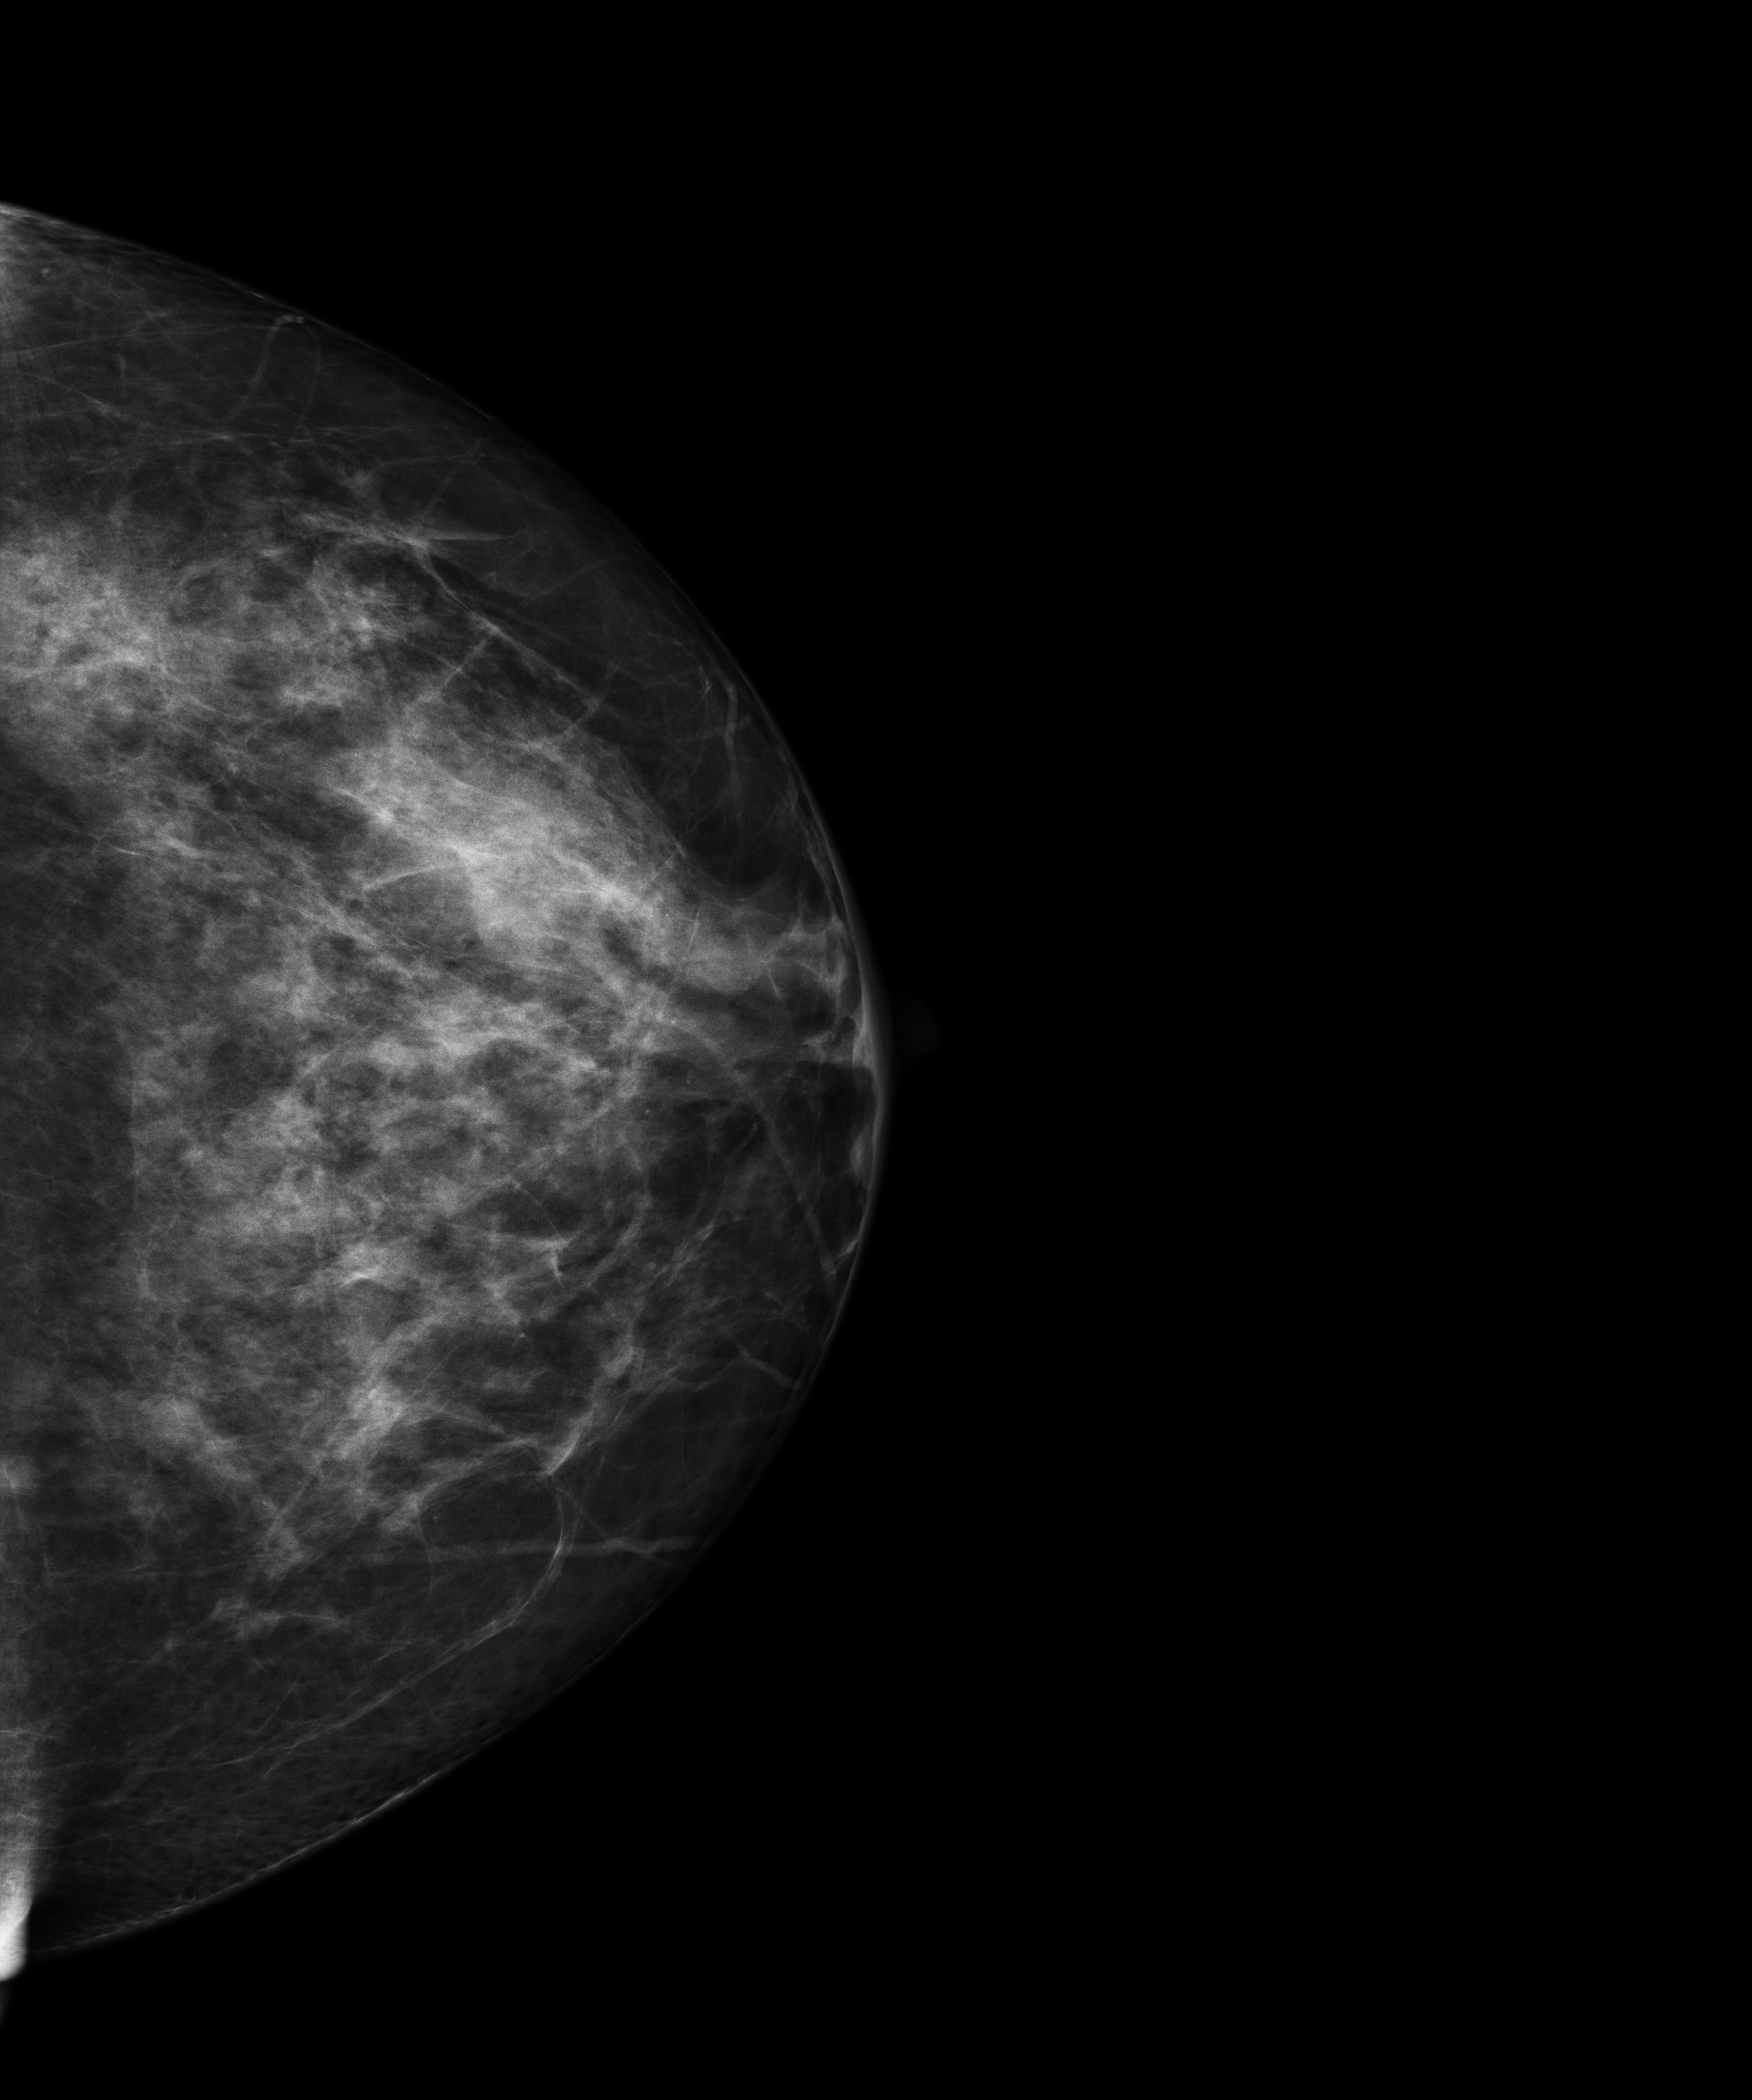
Annual screening mammography examination; compressed breast thickness 67 mm. Female patient, age 45 years.
Image type: full-field digital mammogram. Breast: left. Projection: cranio-caudal projection.